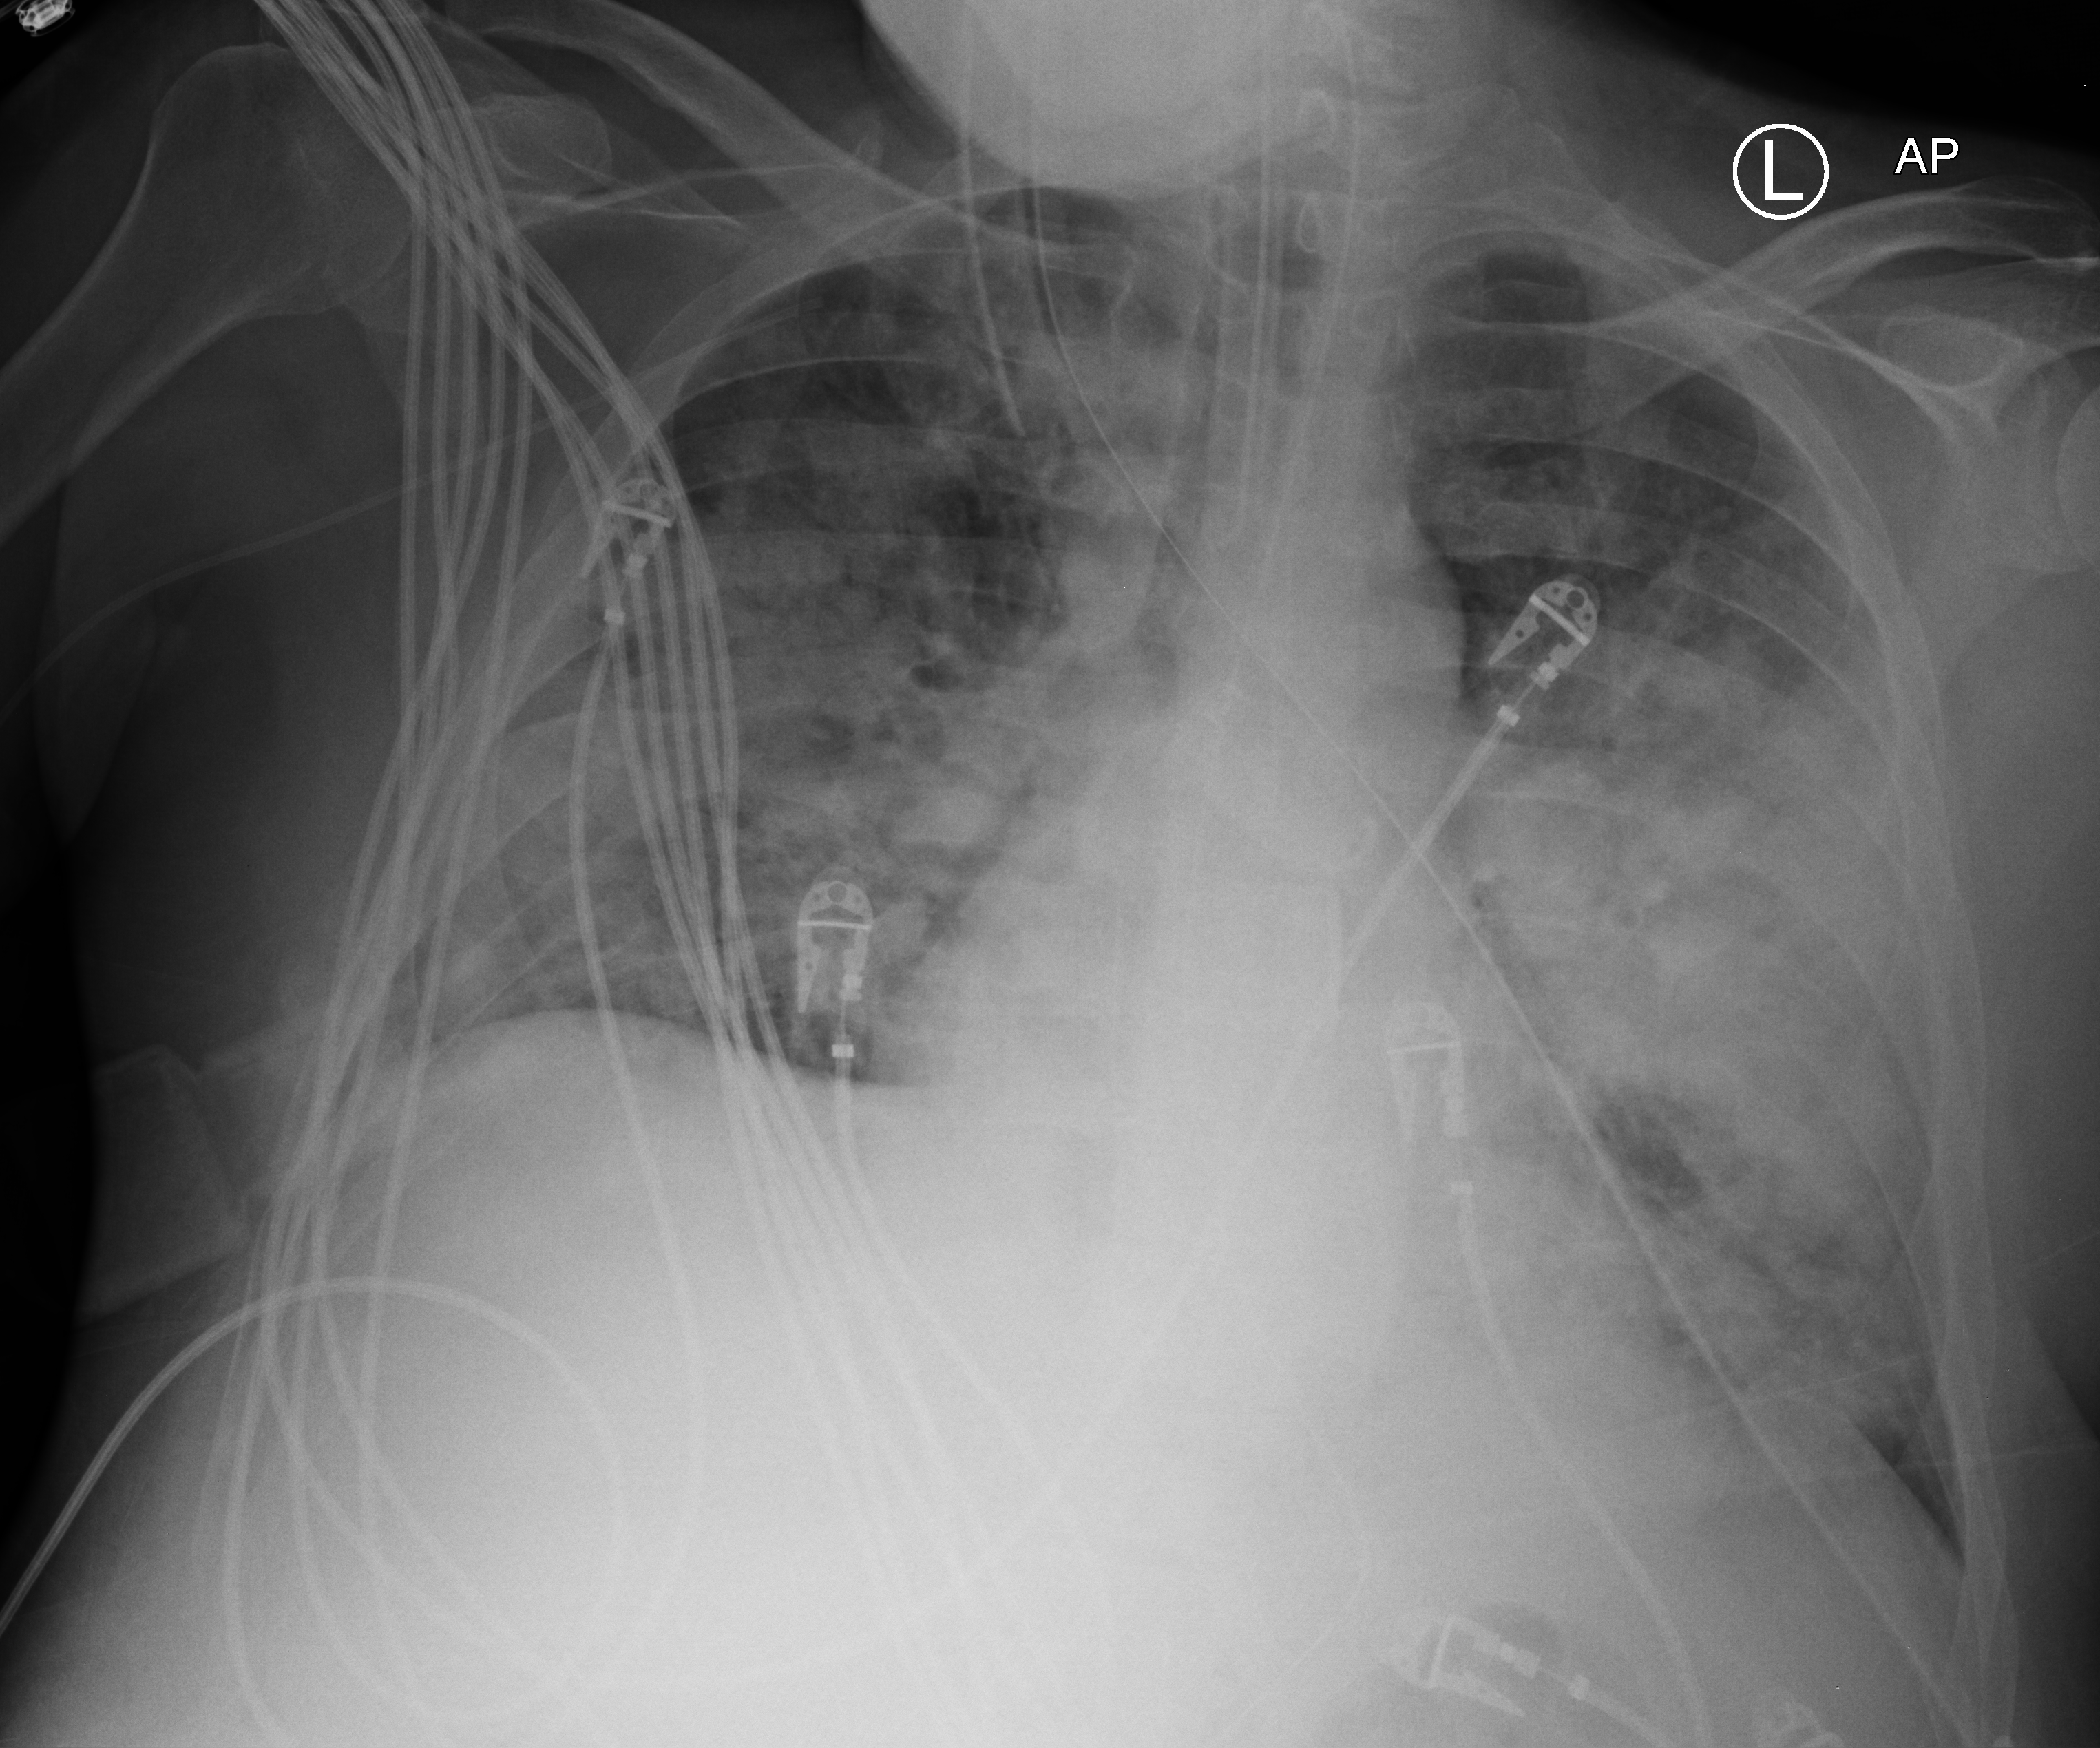
Portable chest radiograph. Male patient hospitalised with COVID-19, age 18–59 years.
From the hospital-stay record, not from the radiograph (when in the stay this image was taken is not recorded): COPD (admission record): no.